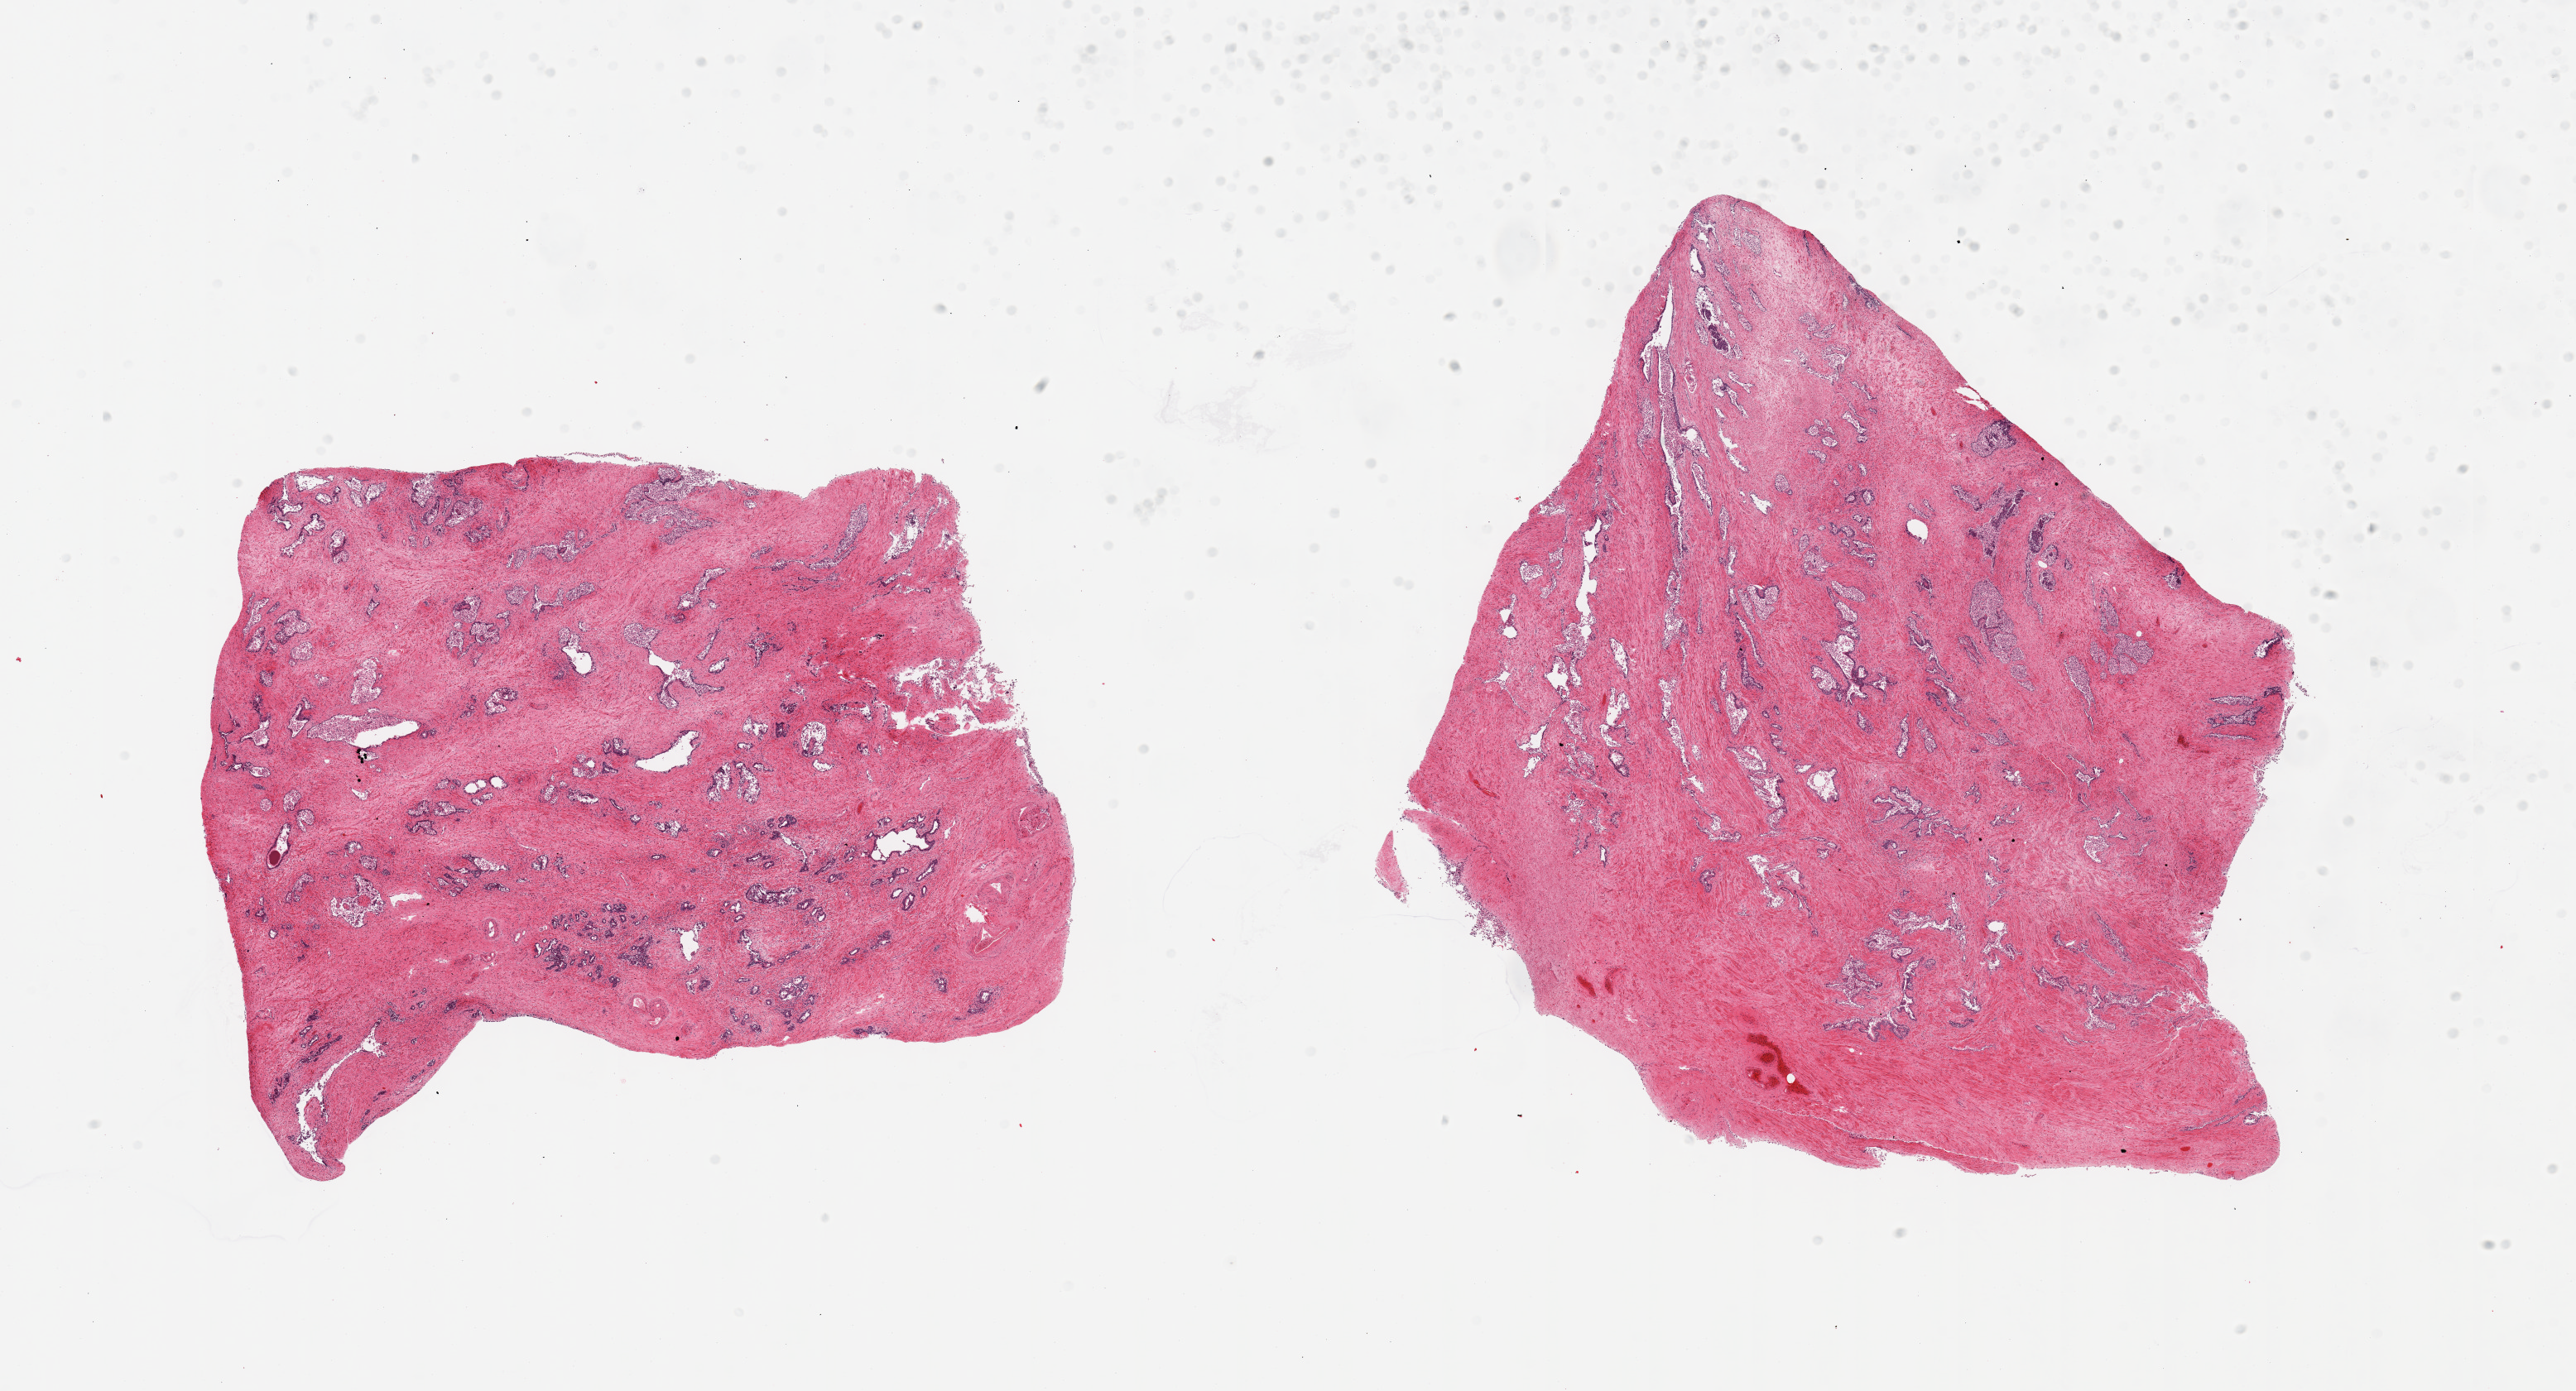
H&E whole-slide image — whole scanned area (about 24.6 x 13.3 mm, acquisition: 20x scan) shown as a low-resolution overview, PAXgene-fixed paraffin-embedded (PFPE) section, sampled site (target tissue): prostate, tissue donor sample.
- review note (as recorded): 2 pieces, glandular elements with moderately advanced autolysis